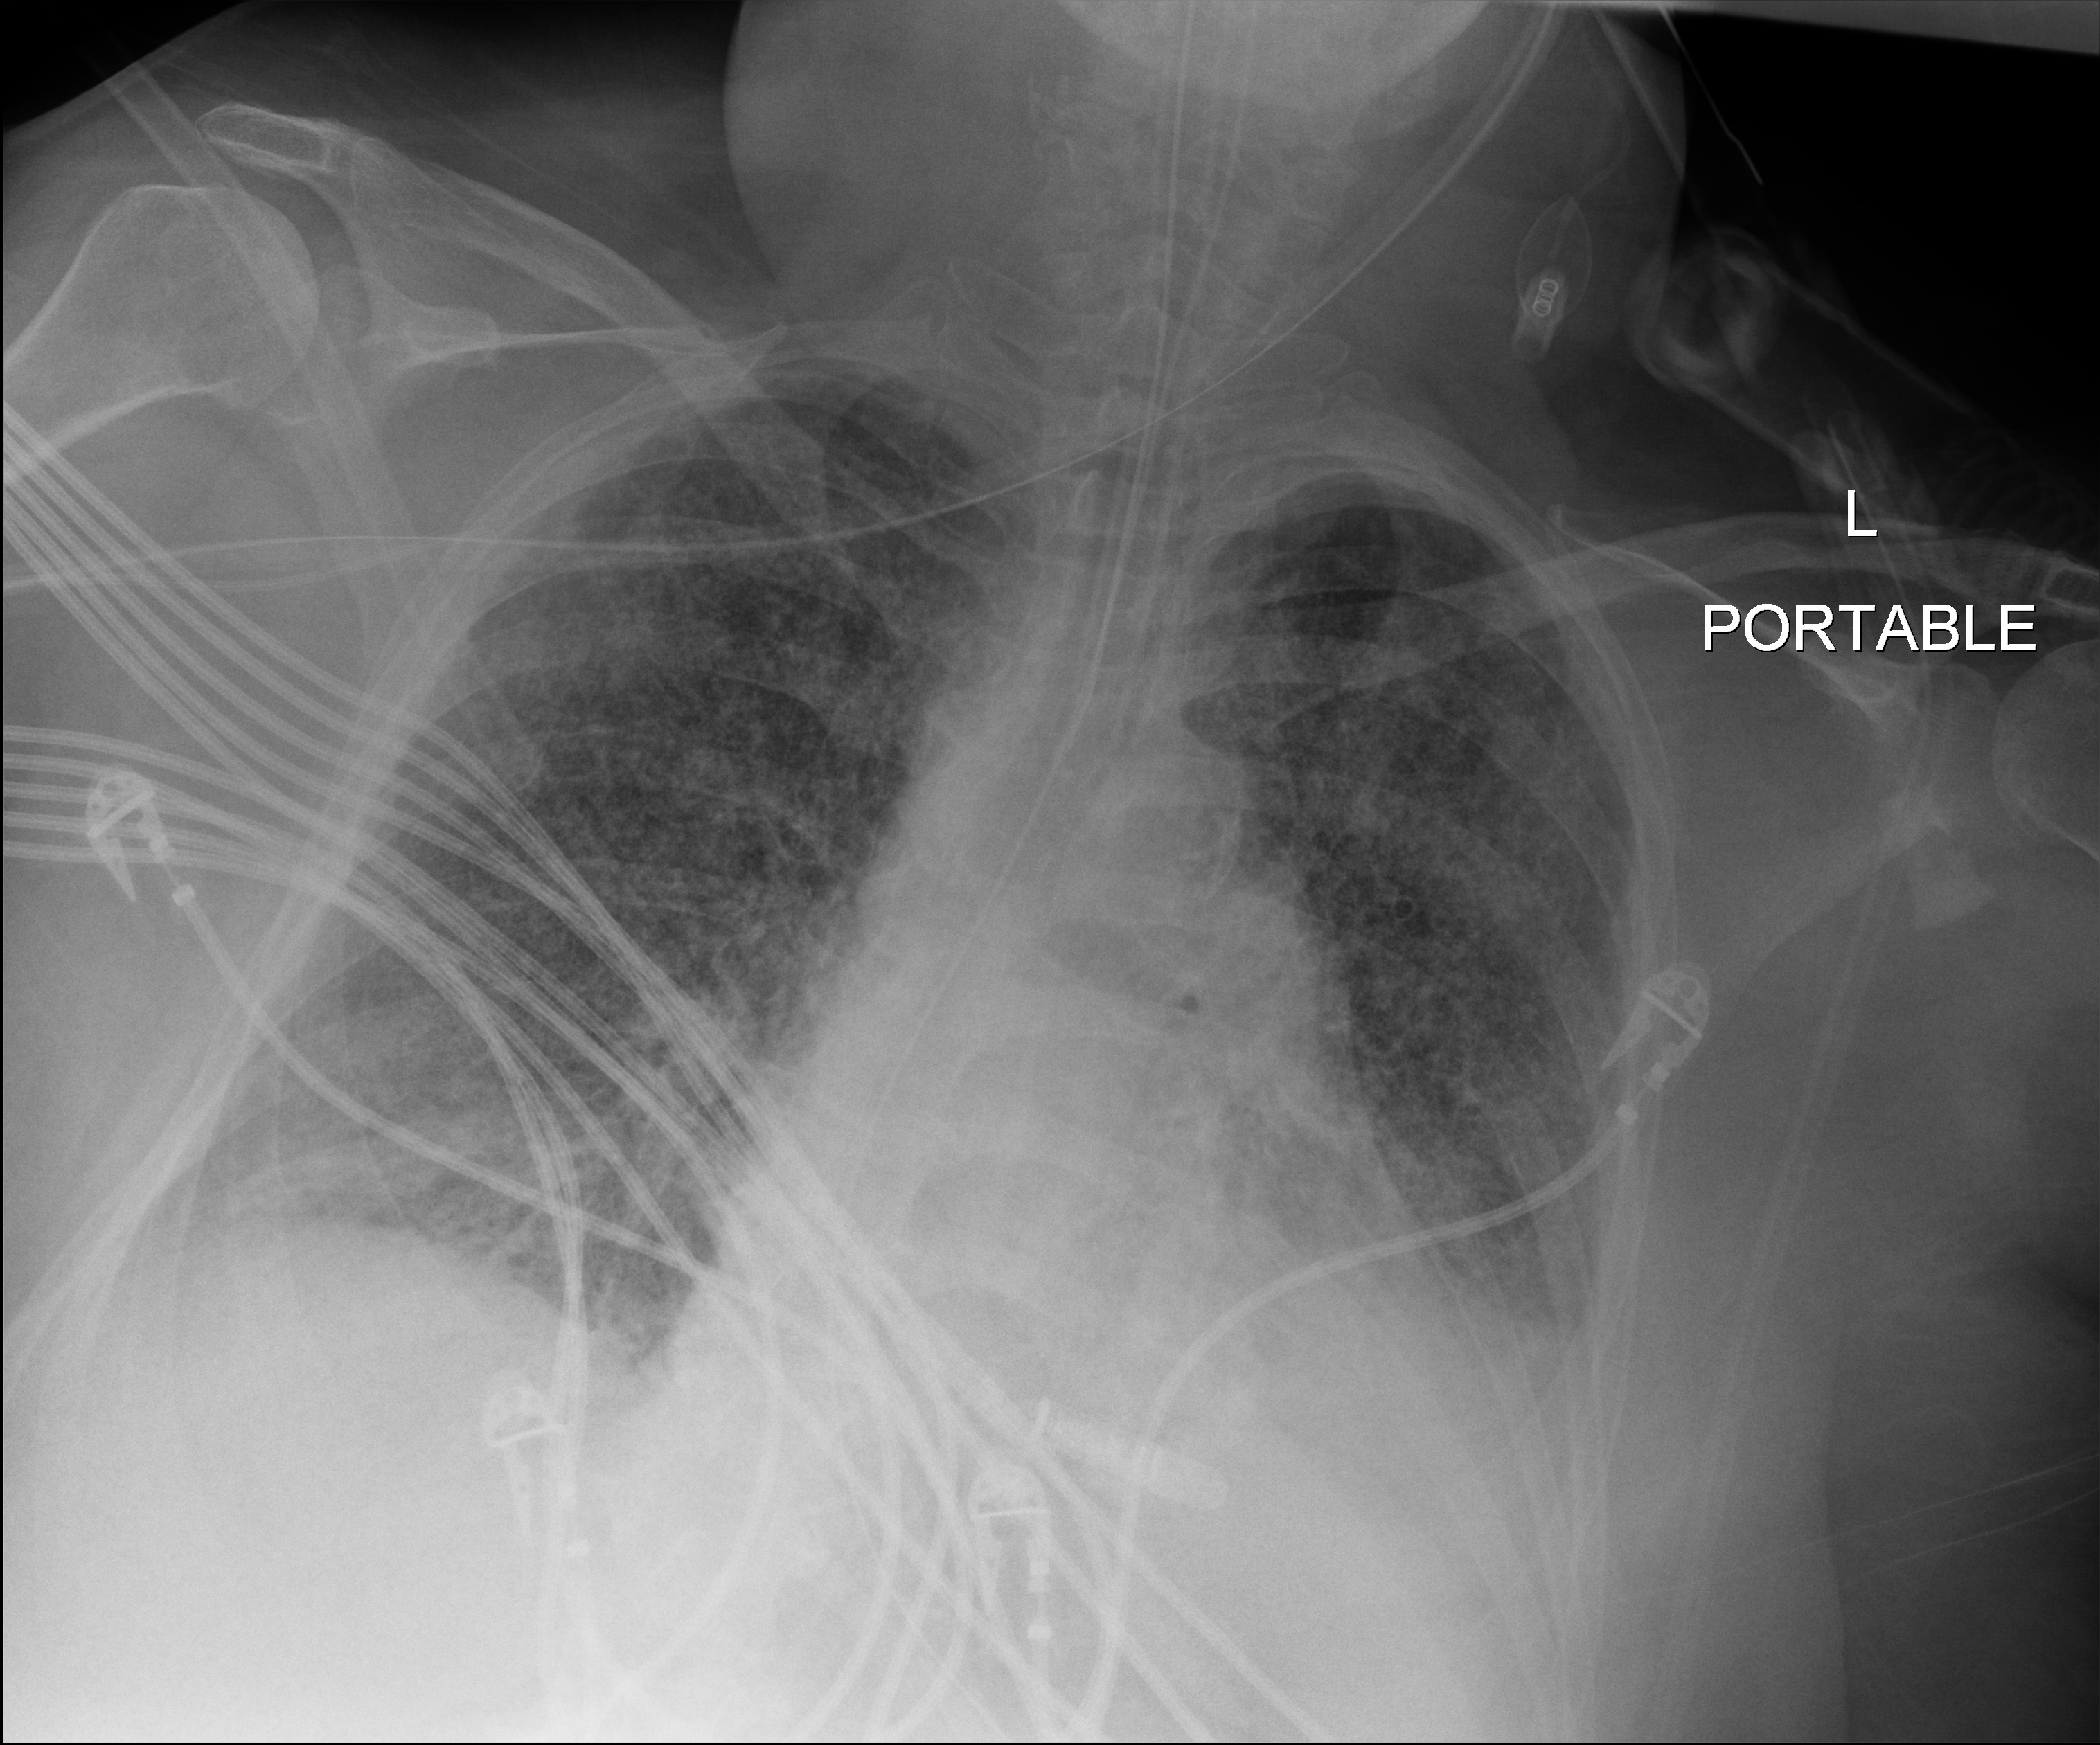
Bedside chest radiograph (digital radiography), anteroposterior (AP) projection. Patient hospitalised with COVID-19; female, aged 60–74 years.
Admission-level facts for this patient (not findings on this image; timing relative to this image not recorded):
- hypertension (admission record): yes